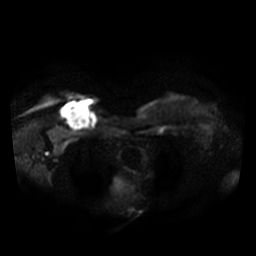
Breast MRI, one axial slice; slice 30 of 36 in the series (ordered by position); diffusion-weighted series; image 2 of 4 stored at this slice position (different b-values; order by instance number); 3 T; 5 mm slice thickness; 256 × 256 image matrix. Female patient.
Outlined on this slice (outlined manually by an expert reader):
- tumour on diffusion-weighted imaging: bounding box [x1, y1, x2, y2] px = [62, 102, 91, 129]